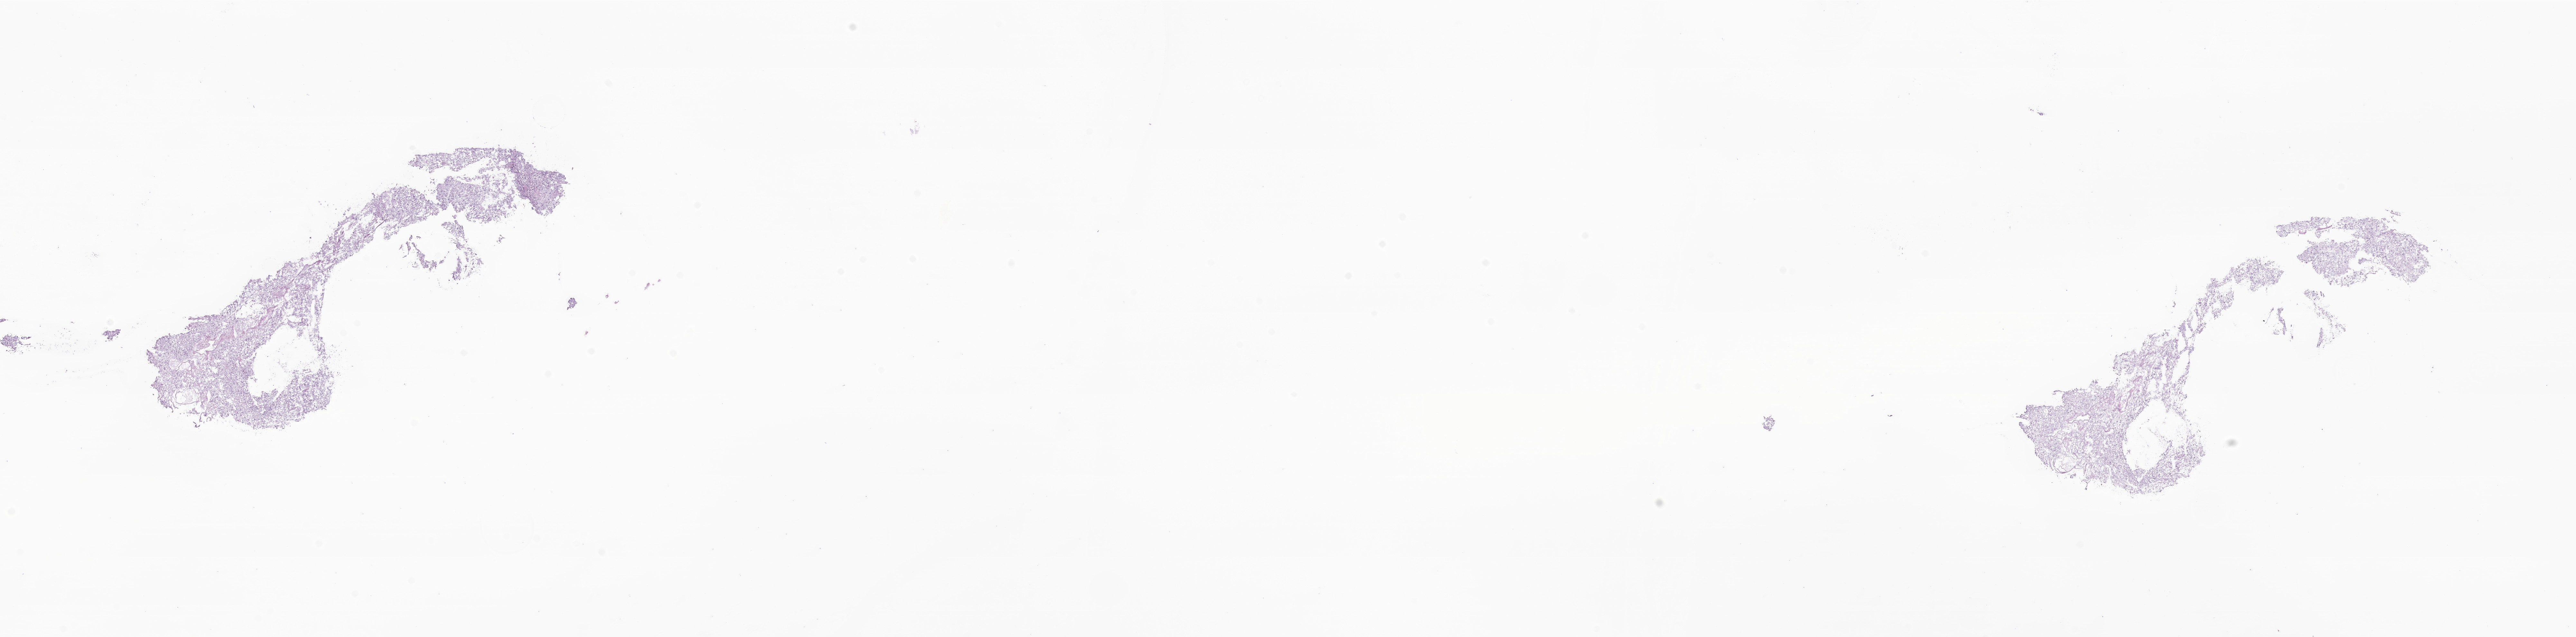
H&E whole-slide image of tumor tissue from the brain — low-resolution overview of the scanned area, about 33.7 x 8.3 mm, frozen section (OCT-embedded). Patient: female, age 186 months (15 years 6 months).
Diagnosis (ICD-O-3 morphology term): Neoplasm, uncertain whether benign or malignant.